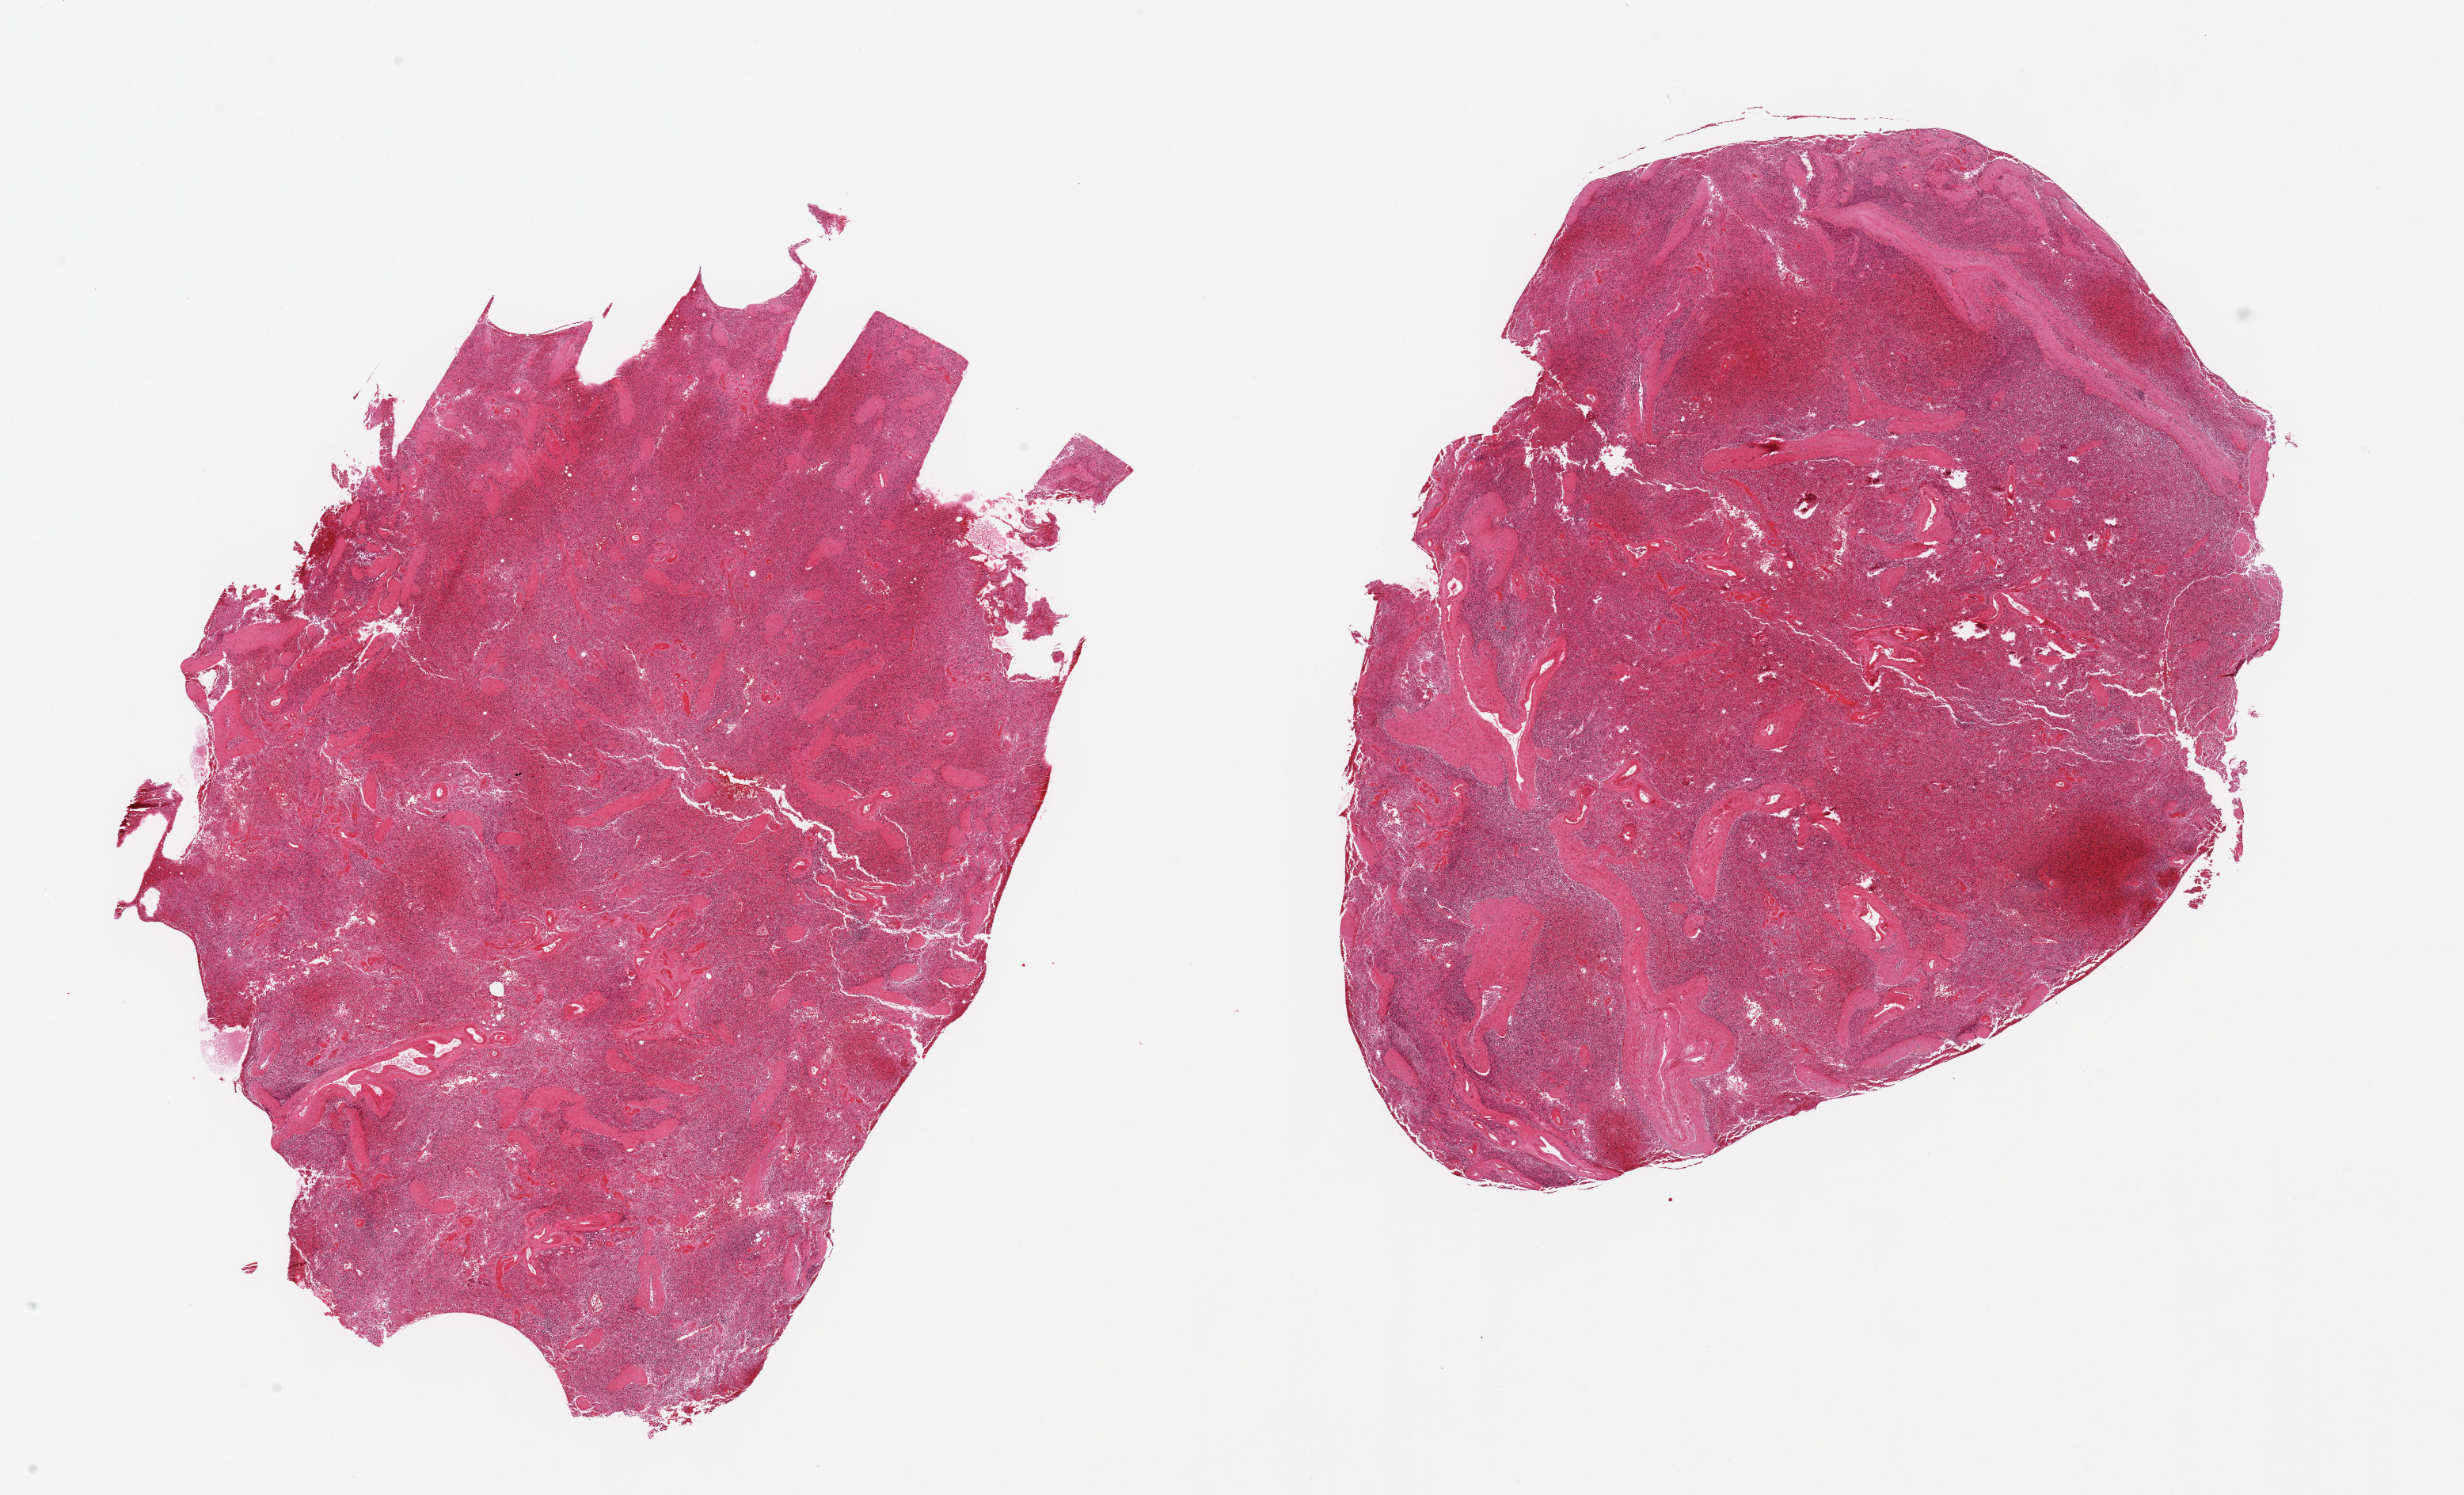
Whole-slide image, H&E stain — a low-resolution overview of the entire scanned area, about 24.6 x 14.9 mm (from a 20x scan); PAXgene-fixed paraffin-embedded (PFPE) section; target tissue: spleen; tissue donor sample. Donor sex: male.
Pathologist's review note for this sample: 2 pieces; severely congested.